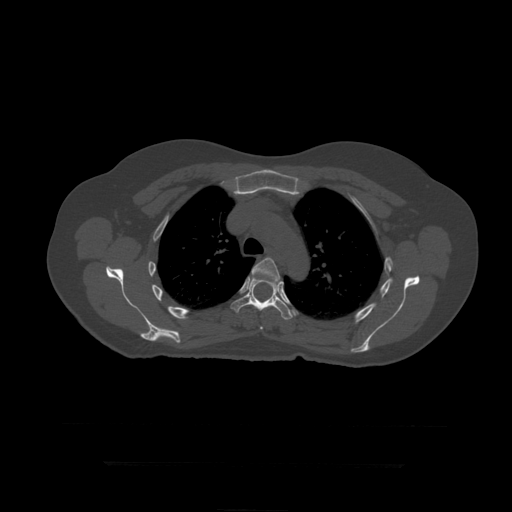
CT including the spine, one axial slice. Slice 325 of 399 in the series (ordered by position). Bone window (W 1800 / L 400 HU). 1.25 mm slice thickness. 512 × 512 image matrix. Patient age 41 years. From the clinical record (not read from this slice): primary cancer: breast.
Structures marked on this image (semi-automatically segmented with operator editing):
- T5 vertebra: box from (x=252, y=258) to (x=281, y=330) px
- T6 vertebra: (x=231, y=278)–(x=299, y=320)